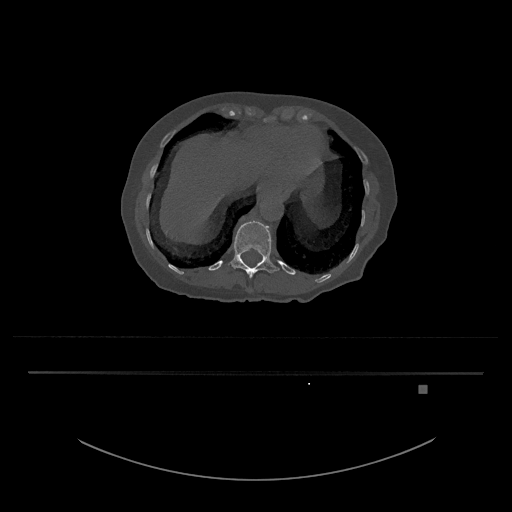
CT including the spine, one axial slice; position 614 of 797 along the scan axis; reconstruction kernel Br40s/3; 120 kVp; bone window (W 1800 / L 400 HU); 512 × 512 image matrix, field of view 500 × 500 mm. Patient: female, 57 years. From the clinical record (not read from this slice): primary cancer: cervical.
Outlined on this slice (semi-automatically segmented with operator editing):
- T12 vertebra: box from (x=230, y=220) to (x=279, y=279) px